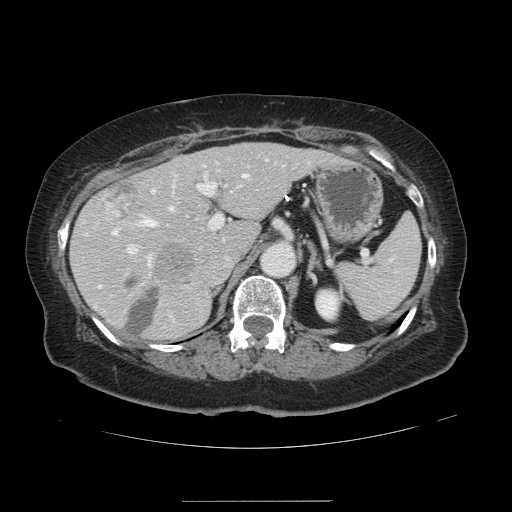
Contrast-enhanced abdominal CT, one axial slice. Slice 83 of 141 in the series (ordered by position). 120 kVp. Intravenous contrast given. Soft-tissue window (W 400 / L 40 HU). 2.5 mm slice thickness. 512 × 512 image matrix, field of view 393 × 393 mm. Female patient, age 74 years. Case-level facts recorded for this patient, not image findings: diagnosis: colorectal cancer liver metastases, imaged before liver resection; multiple liver metastases: yes; largest metastasis: 7 cm.
Outlined on this slice (outlined manually by an expert reader):
- hepatic veins: box from (x=113, y=173) to (x=247, y=234) px
- liver: (x=72, y=144)–(x=332, y=341)
- planned liver remnant (the part of the liver to remain after resection): (x=72, y=144)–(x=332, y=340)
- portal vein (with intrahepatic branches): (x=127, y=159)–(x=266, y=265)
- liver metastasis: (x=99, y=174)–(x=146, y=217)
- liver metastasis: (x=126, y=279)–(x=161, y=335)
- liver metastasis: (x=157, y=243)–(x=195, y=279)